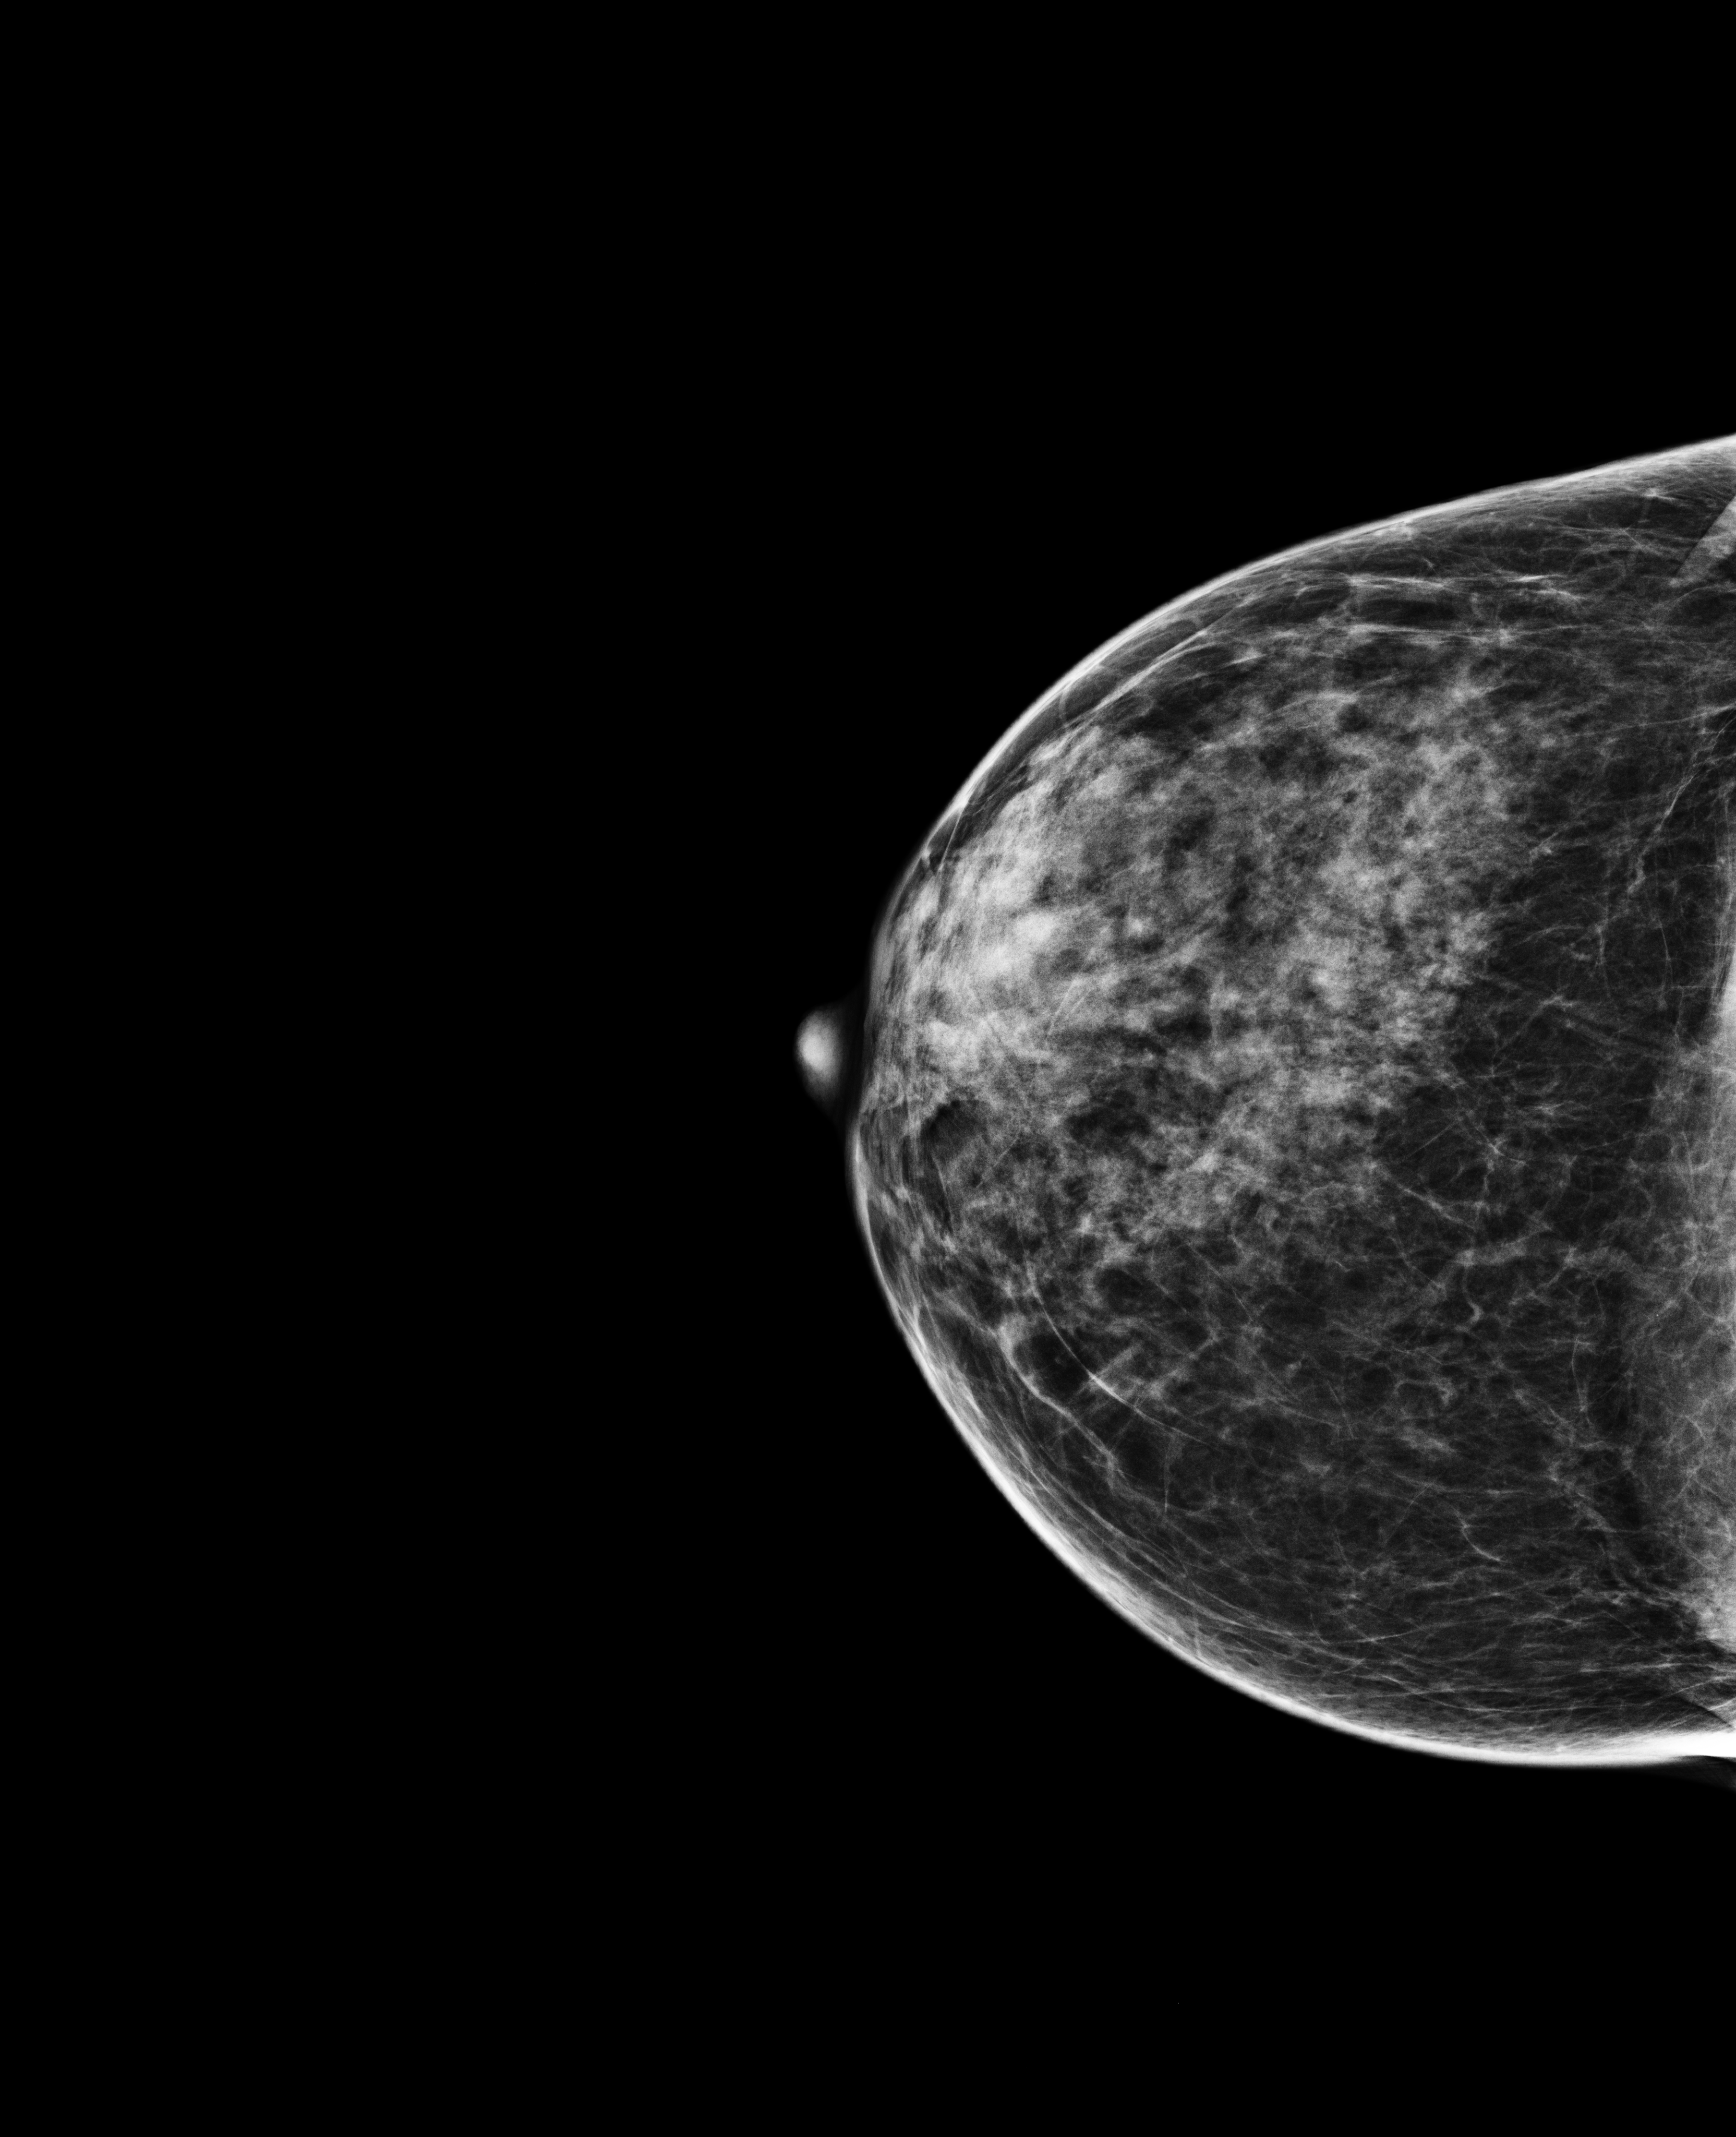
Annual screening mammography examination; system: Selenia Dimensions. Female patient, age 51 years.
Image type: full-field digital mammogram. Breast: right. Projection: cranio-caudal projection.